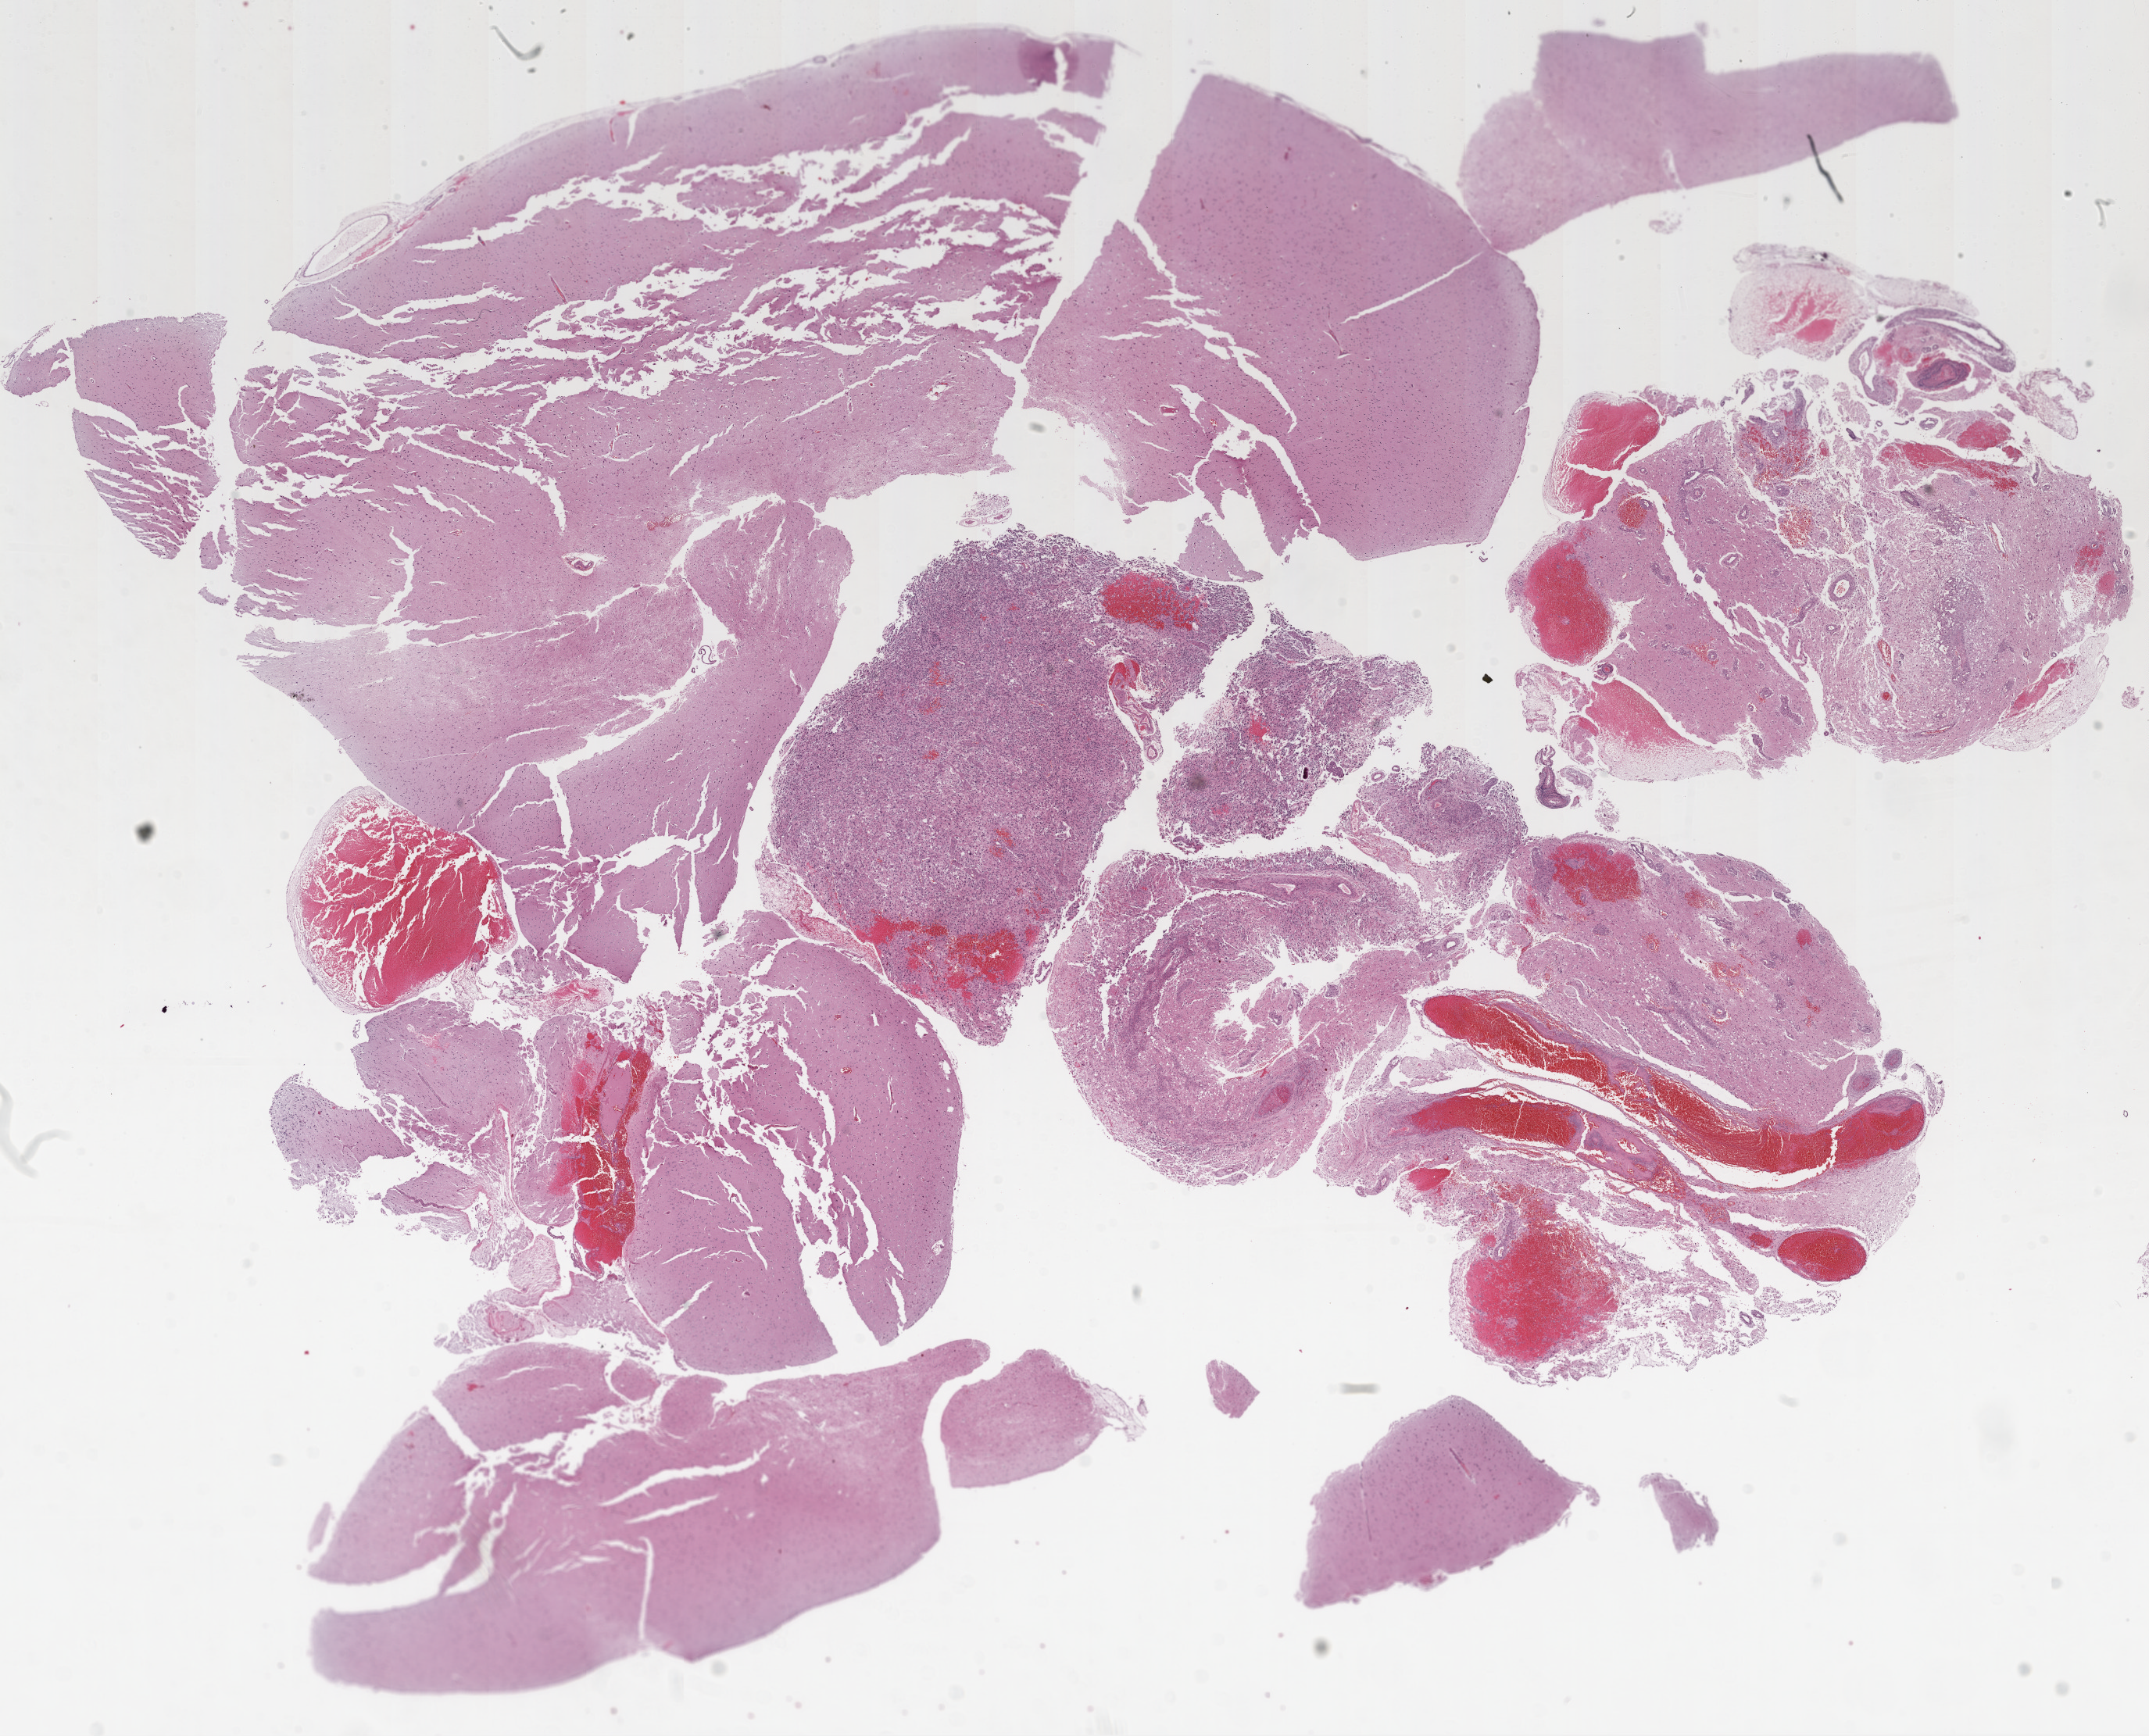
H&E-stained whole-slide image — low-resolution overview of the scanned area, about 22.1 x 17.8 mm; formalin-fixed paraffin-embedded (FFPE) diagnostic section; primary tumour sample from the brain. Female patient; age at initial diagnosis 54 years.
Histologic diagnosis: Glioblastoma.